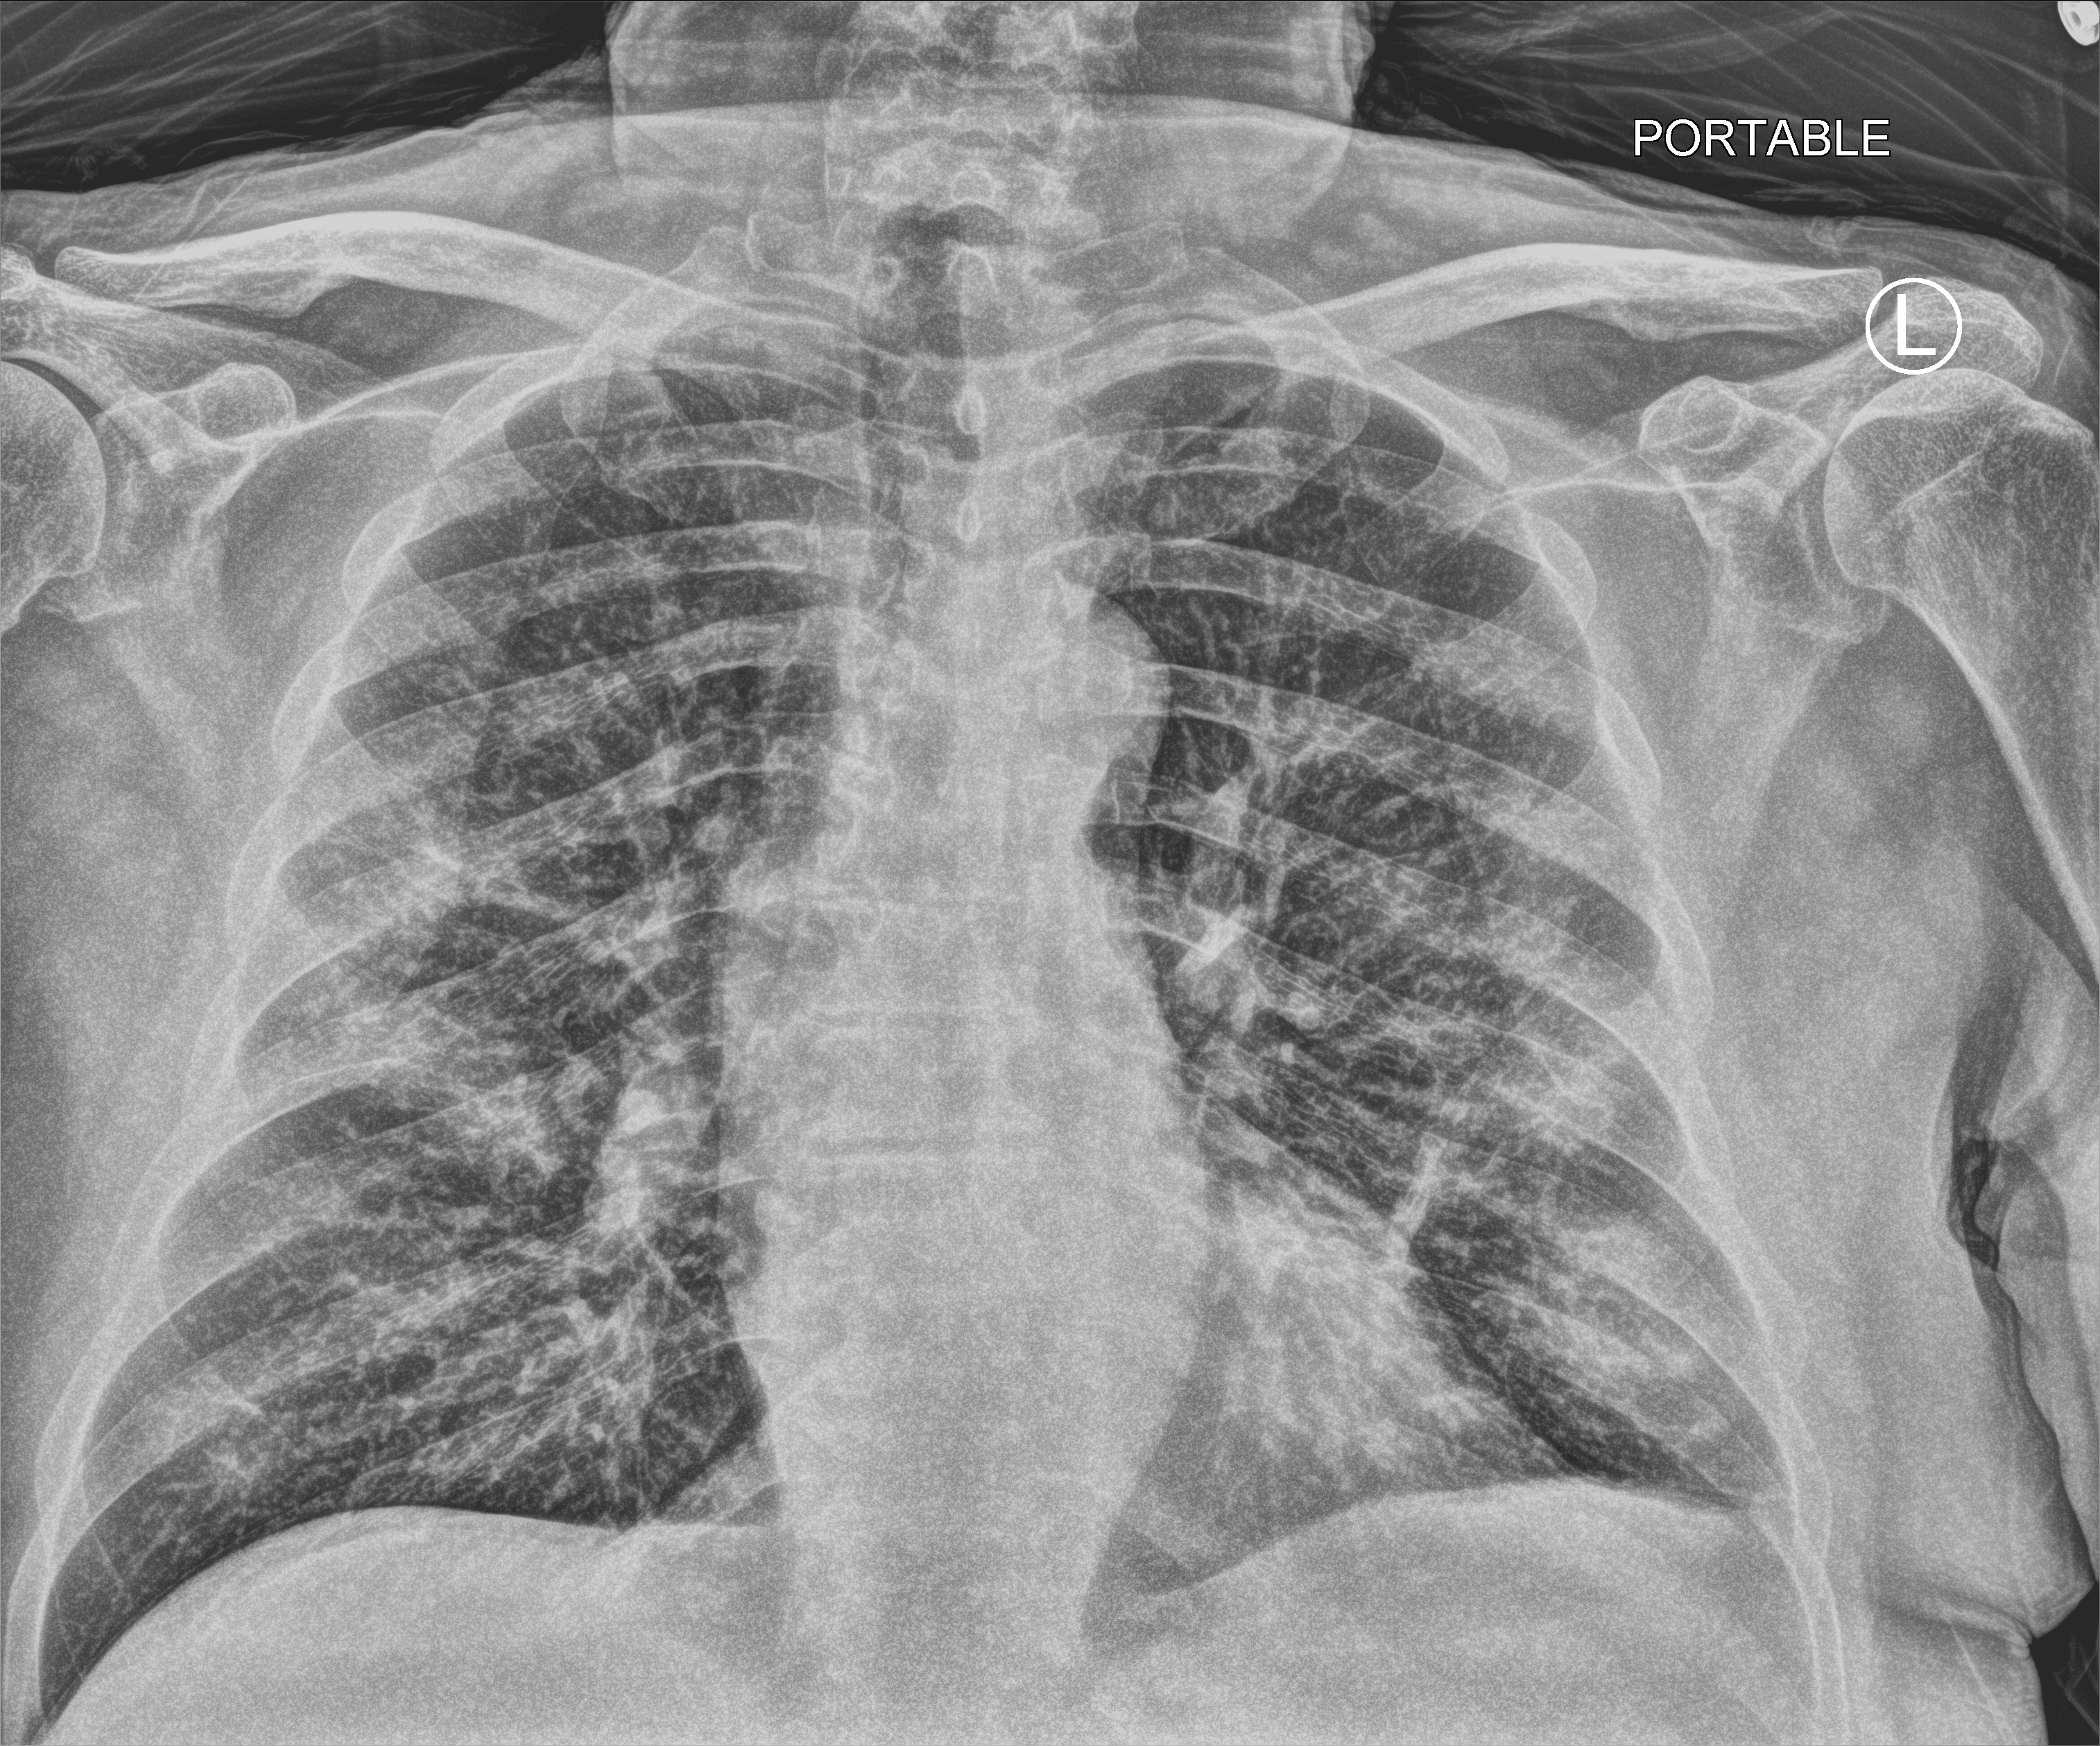
Portable chest radiograph; anteroposterior (AP) projection. Male patient hospitalised with COVID-19, age 60–74 years.
Hospital-stay facts (about this admission, not read from this image; timing relative to this image not recorded): mechanically ventilated during this hospital stay: yes; other chronic lung disease (admission record): no; diabetes (admission record): no.